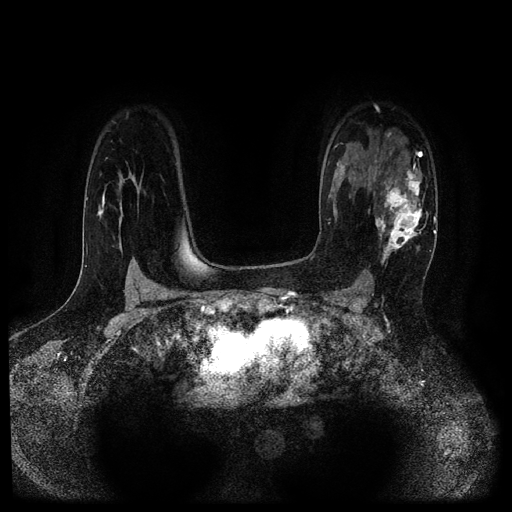
Breast MRI (dynamic contrast-enhanced, multi-phase), one axial slice; slice 74 of 116 in the series (ordered by position); dynamic contrast-enhanced series, time point 2 of 5 at this slice position (early post-contrast); 1.5 T; TE 2.7 ms, TR 5.4 ms; 2.2 mm slice thickness; 512 × 512 image matrix, field of view 330 × 330 mm. Patient: female, 43 years.
Annotated regions visible in this slice (semi-automatic segmentation, software-assisted and operator-edited):
- breast lesion (labelled 'tumour' in the annotation; benign lesions carry a separate 'benign' label): bounding box <369,163,429,268> (left, top, right, bottom; pixels)